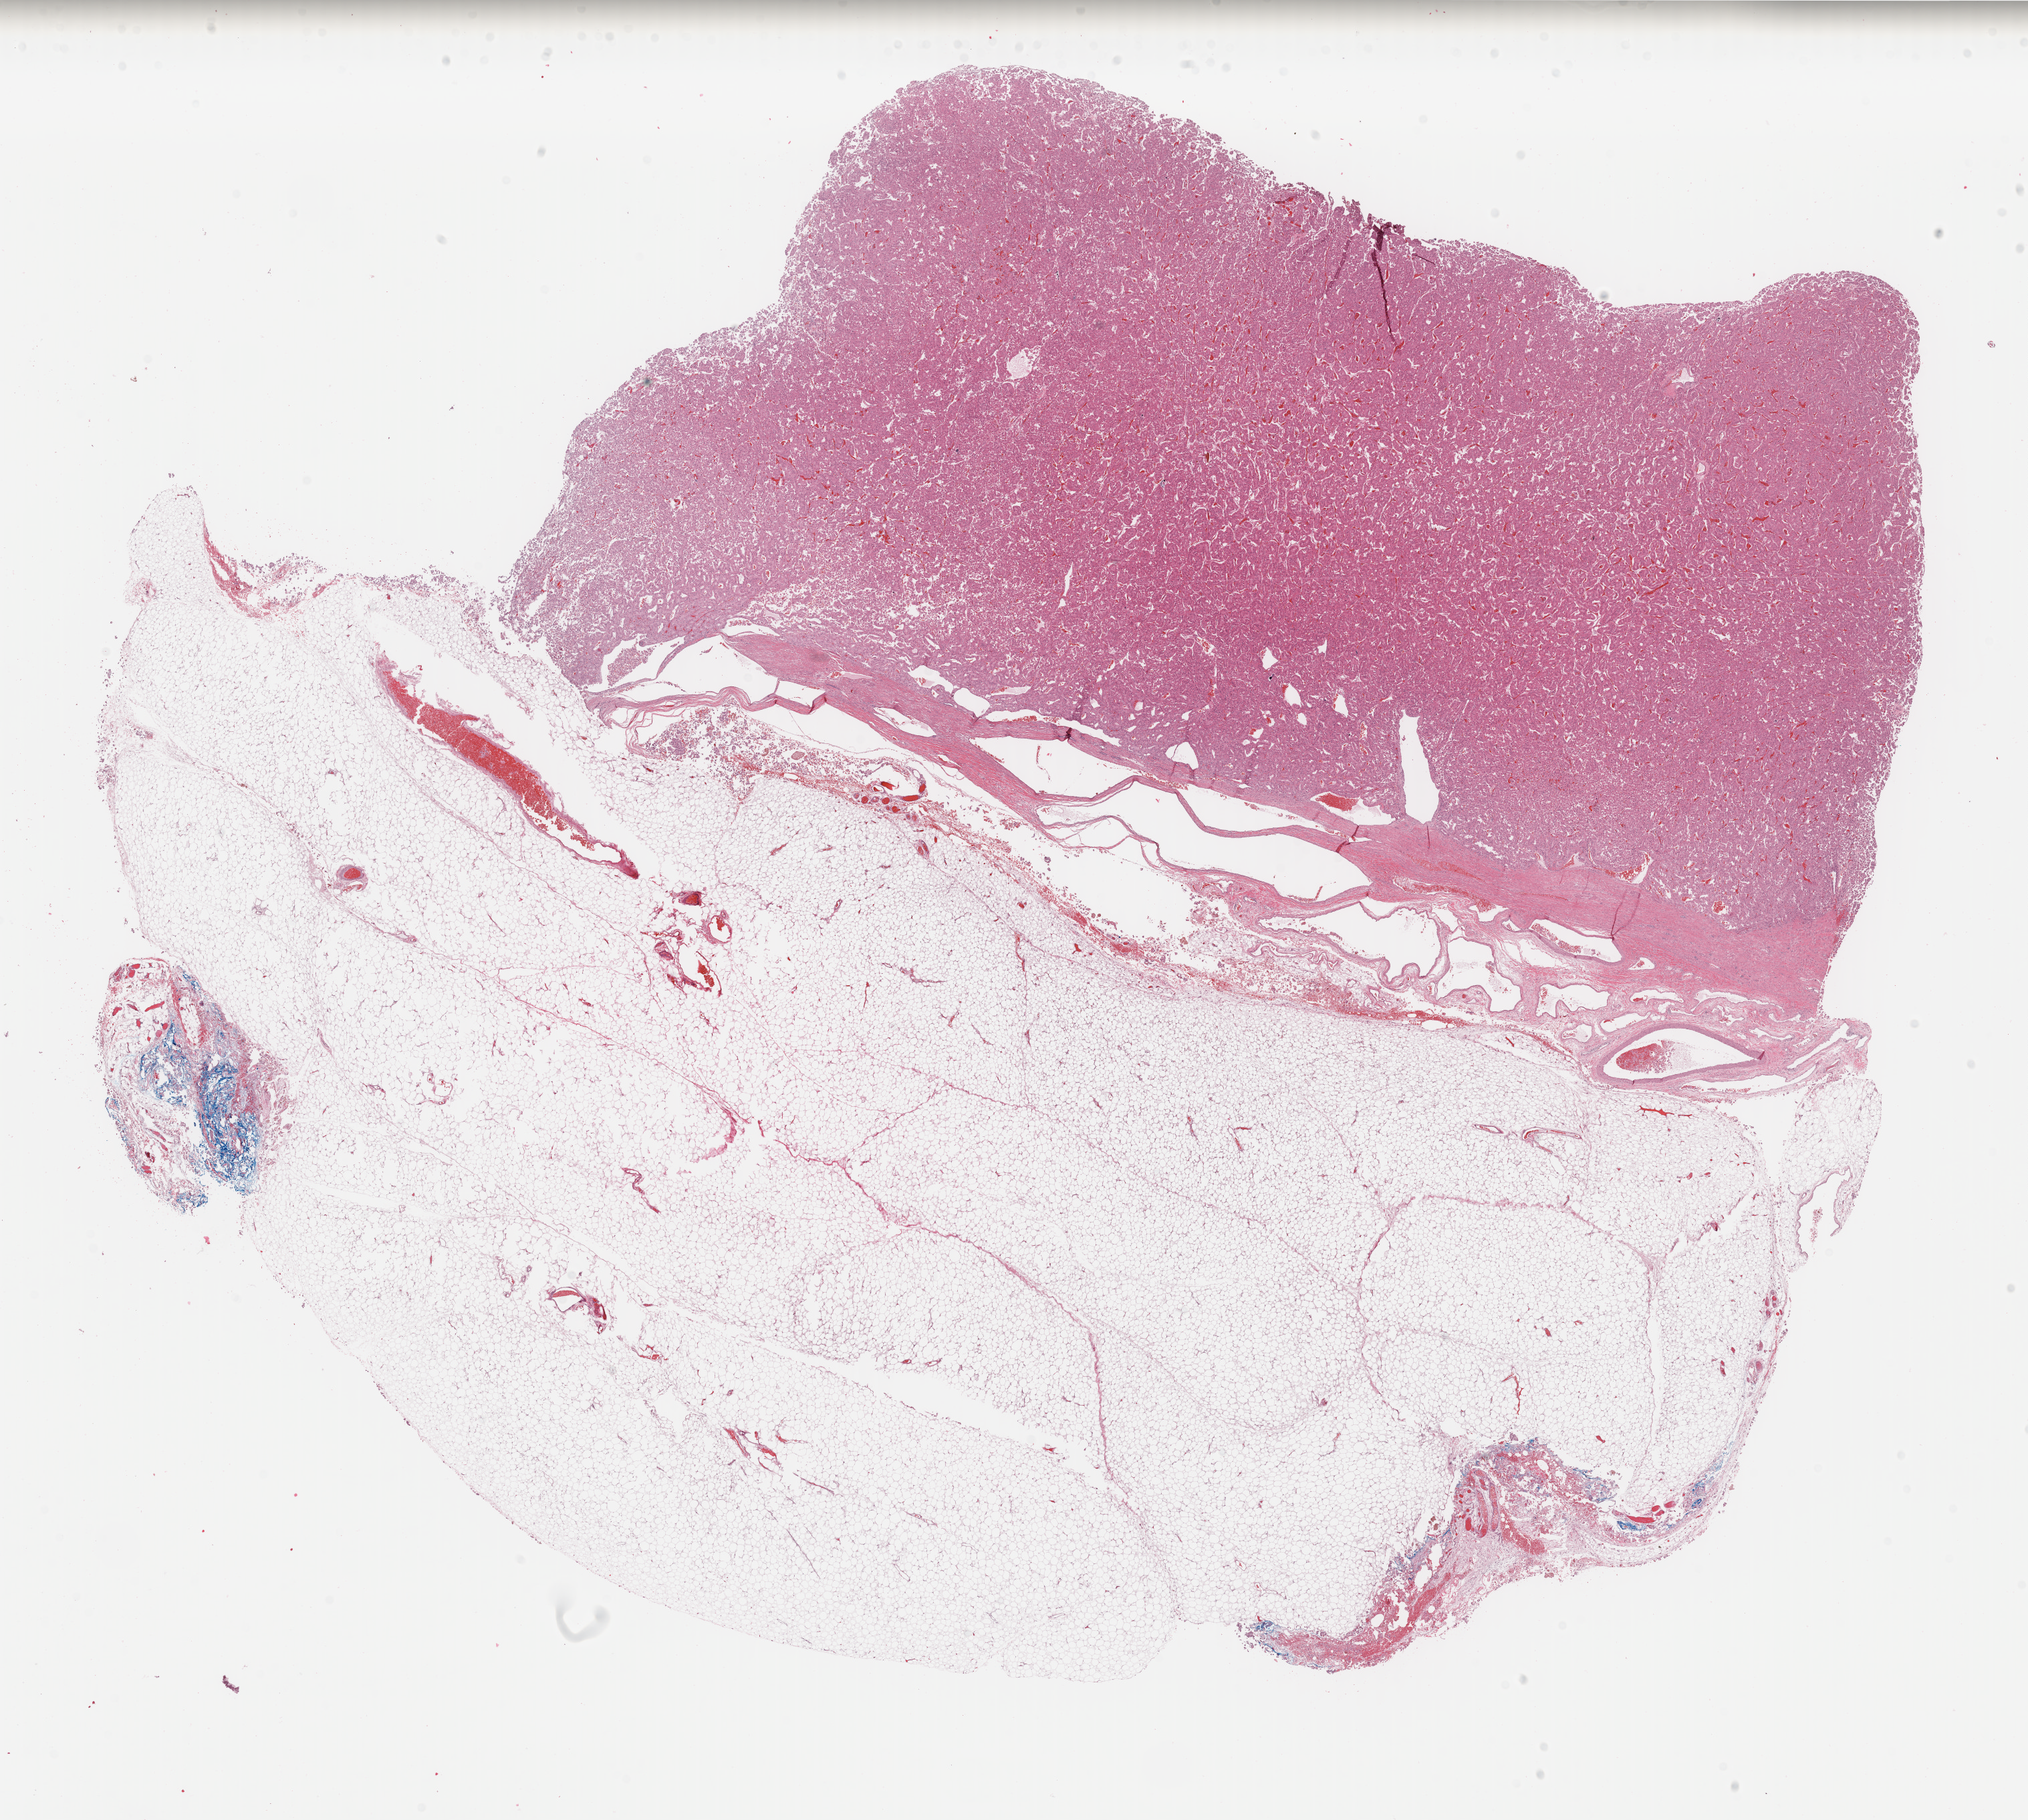
H&E-stained whole-slide image — low-resolution overview of the scanned area, about 24.0 x 21.5 mm. Formalin-fixed paraffin-embedded (FFPE) diagnostic section. Kidney, primary tumour sample. Patient: male, age at initial diagnosis 45 years. Pathologist review of this section (percent, as recorded): tumour cells 50%, tumour nuclei 60%, normal cells 50%, stromal cells 0%, necrosis 0%. Infiltration values recorded for this section: lymphocyte infiltration 0%, monocyte infiltration 0%, neutrophil infiltration 0%.
Laterality: right. TNM: T2a NX. AJCC pathologic stage: II. Diagnosis: Renal cell carcinoma, chromophobe type.